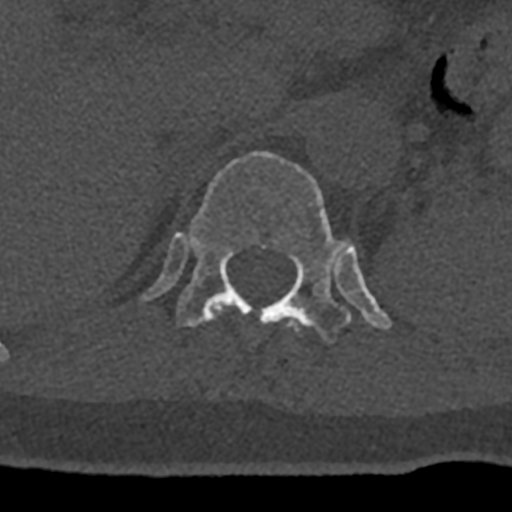
CT including the spine, one axial slice. Position 502 of 797 along the scan axis. Bone window (W 1800 / L 400 HU). 0.5 mm slice thickness. 512 × 512 image matrix. Patient: male, 74 years. From the clinical record (not read from this slice): primary cancer: renal; vertebrae with lytic lesions (as recorded): T10, L1, L2, L3, L4, L5.
Structures marked on this image (semi-automatically segmented with operator editing):
- T11 vertebra: bounding box <213,305,299,331> (left, top, right, bottom; pixels)
- T12 vertebra: <142,151,391,343>